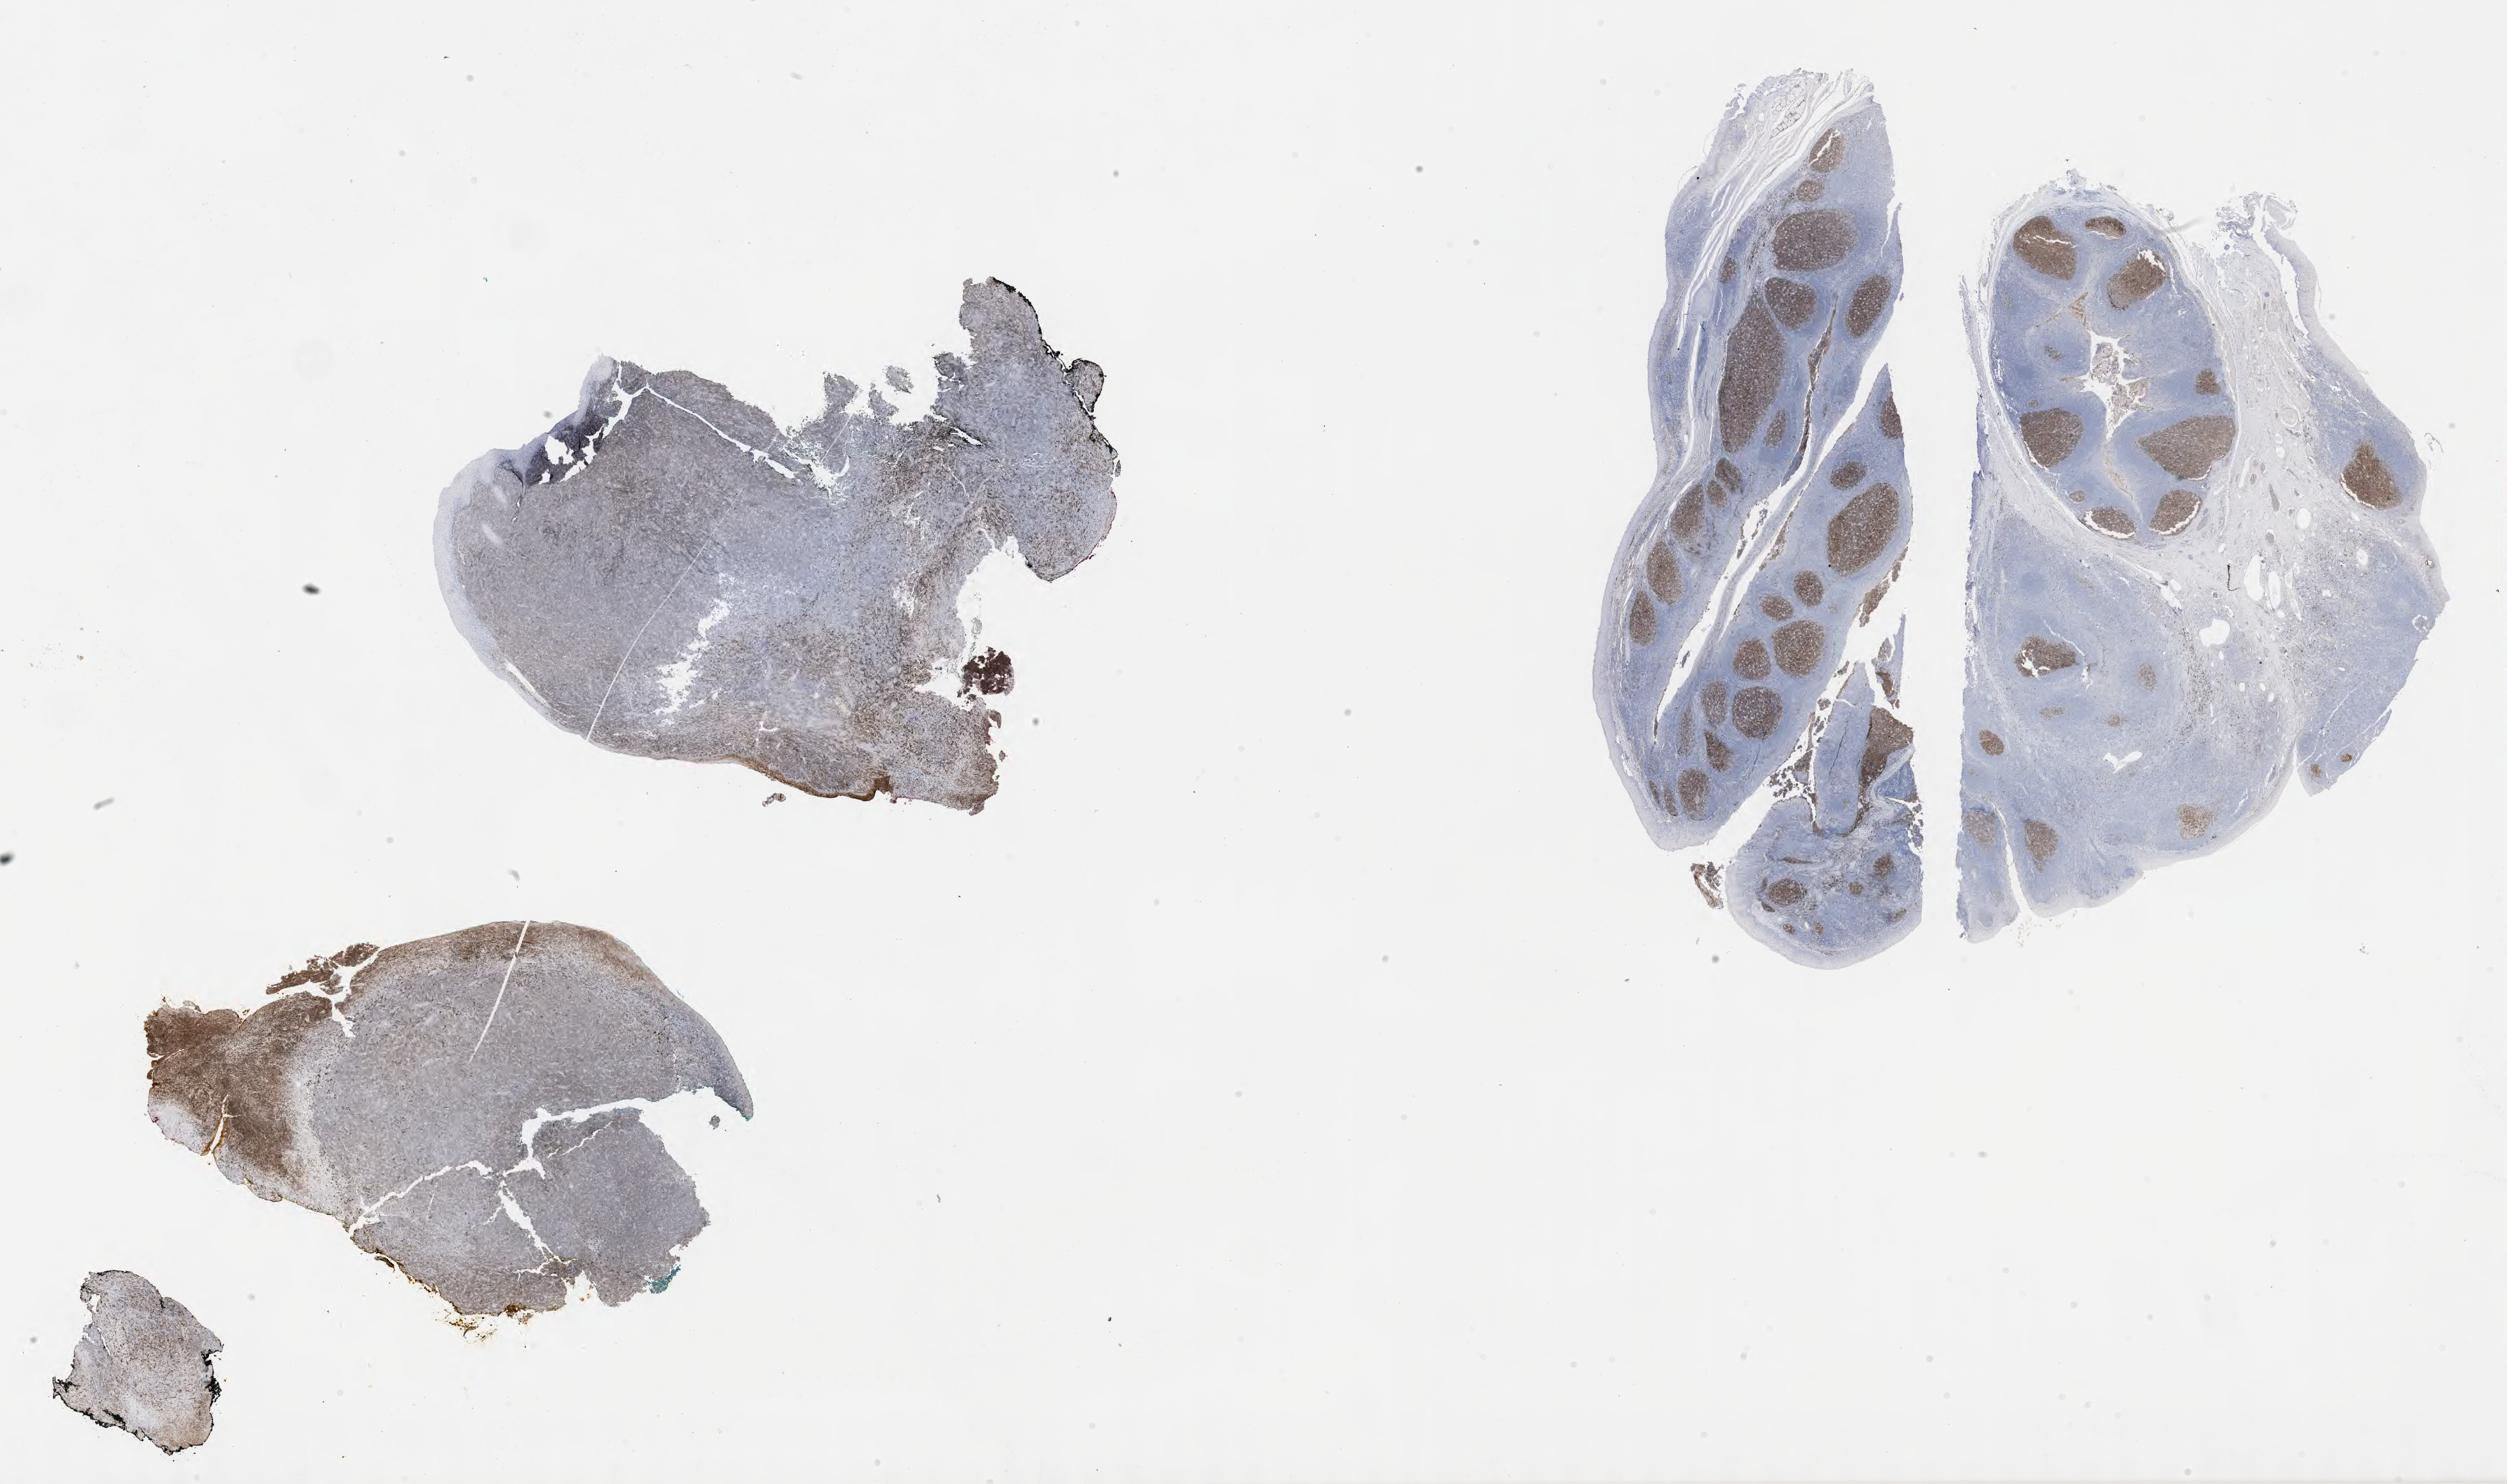
IHC for CD10, whole-slide image, low-resolution overview of the scanned area, about 31.7 x 18.8 mm, specimen: tumor tissue. Male patient, age 49 years.
Diagnosis: Diffuse large B-cell lymphoma, NOS.